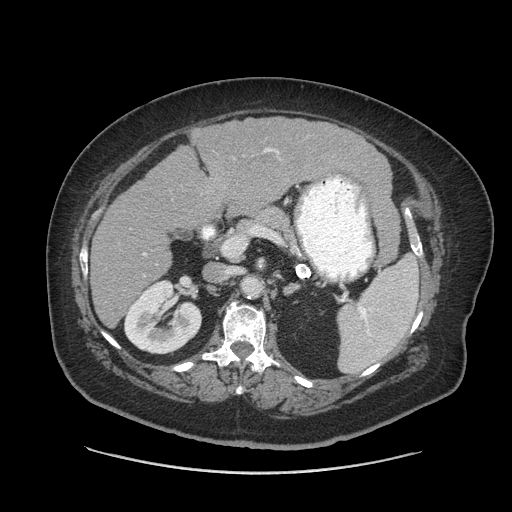
Contrast-enhanced abdominal CT (liver protocol), one axial slice; slice 38 of 91 in the series (ordered by position); 140 kVp; soft-tissue window (W 400 / L 40 HU); 512 × 512 image matrix. From the clinical record (not read from this slice): diagnosis: hepatocellular carcinoma (patient treated with transarterial chemoembolisation; whether this scan precedes or follows treatment is not stated here); TNM stage (as recorded): Stage-I; Child-Pugh class: A; tumour differentiation: well differentiated; tumour nodularity: uninodular.
Structures marked on this image (semi-automatically segmented with operator editing):
- liver parenchyma outside the tumour (the mass and vessels are separate outlines, so this box may not span the whole liver): bounding box <90,116,390,328> (left, top, right, bottom; pixels)
- liver vessels: <144,148,279,255>